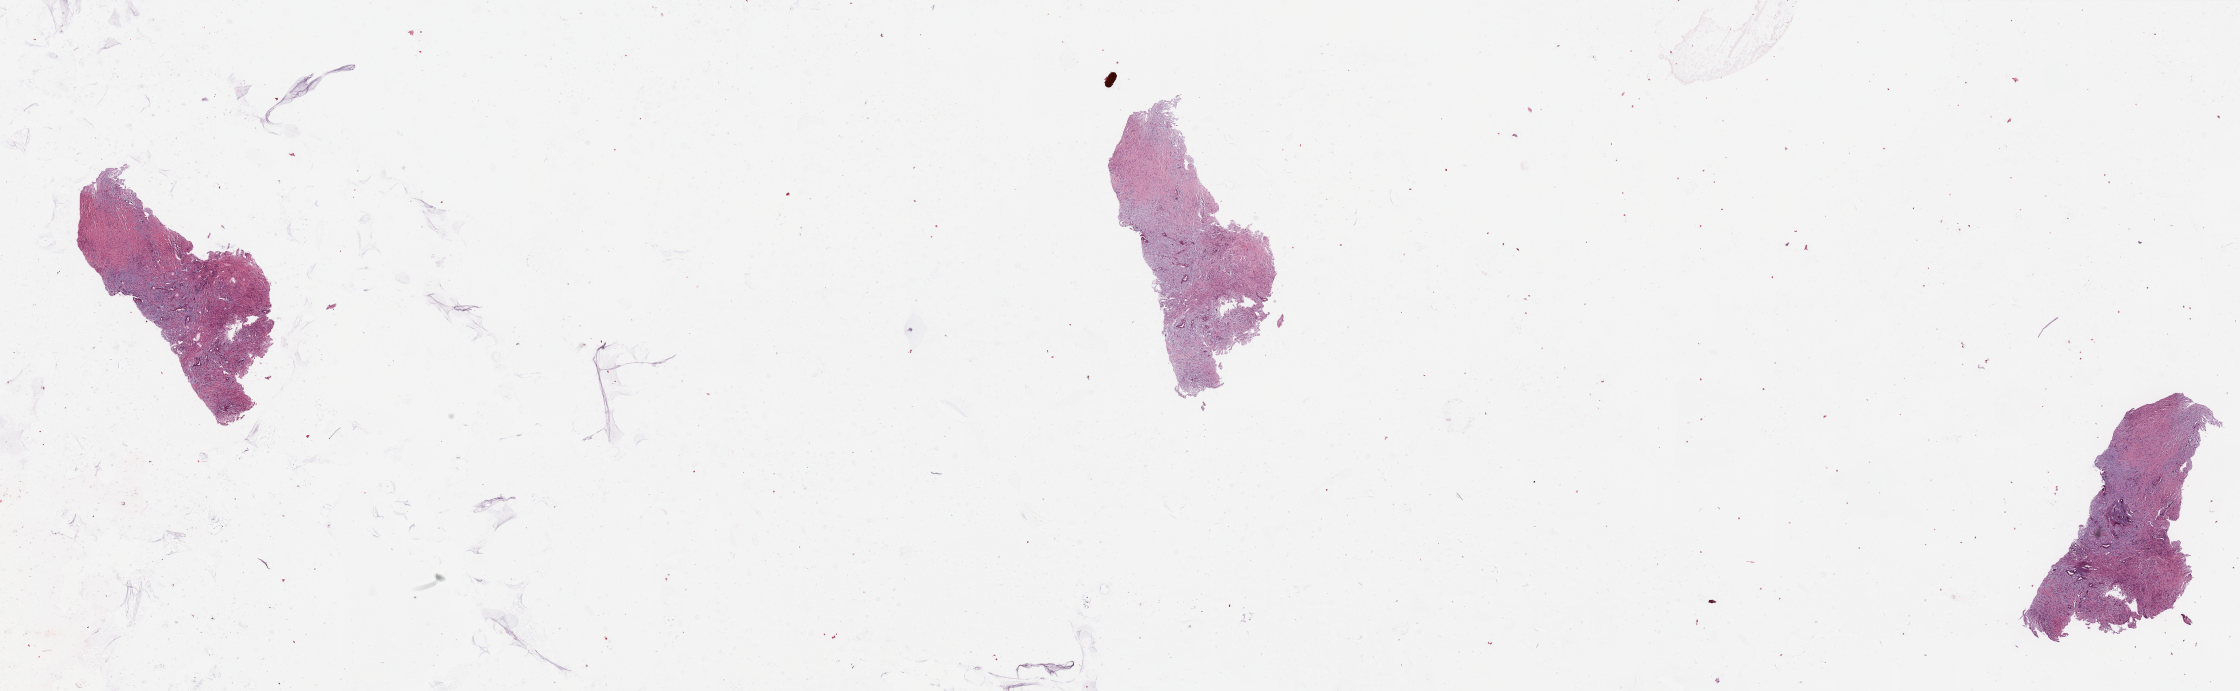
Whole-slide histology image, H&E — whole scanned area (about 35.4 x 10.9 mm) shown as a low-resolution overview. Tumour tissue sample, pancreas. 42-year-old male patient.
Patient diagnosis (cohort enrolment): ductal adenocarcinoma (pancreas). Primary tumour site (as recorded): head.